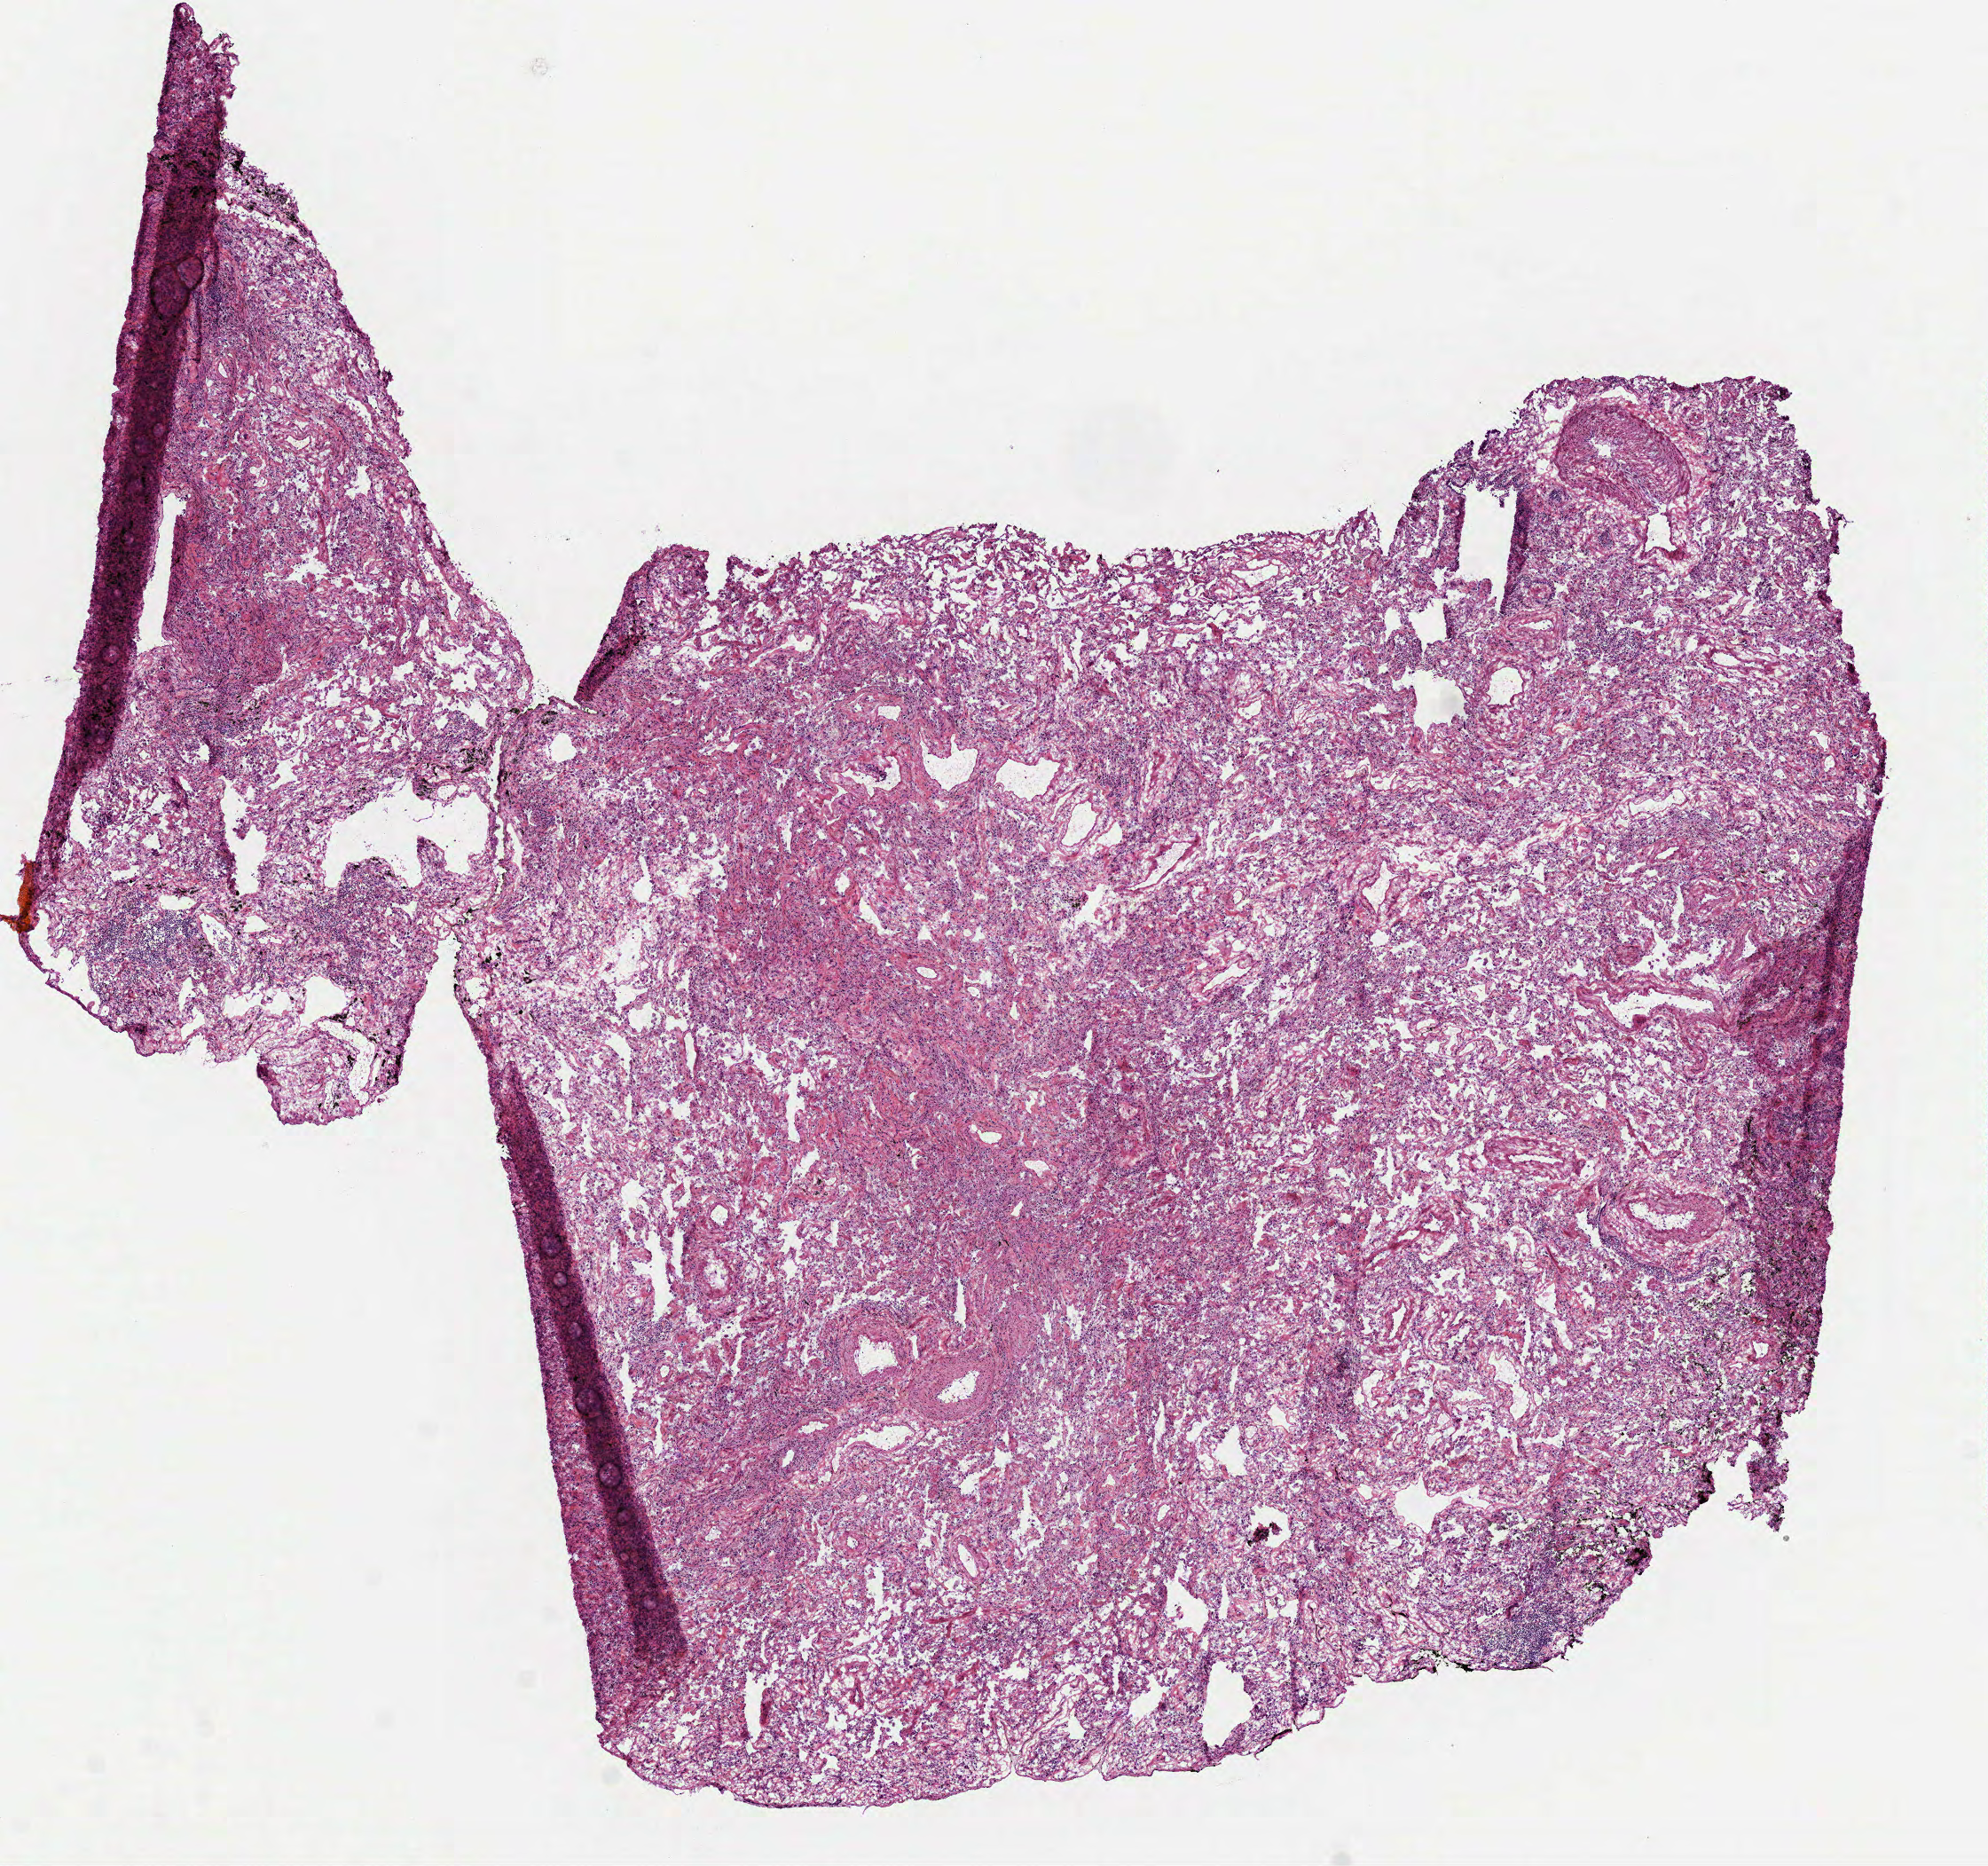
H&E whole-slide image, a low-resolution overview of the entire scanned area, about 9.0 x 8.5 mm (acquisition: 40x scan), frozen section from the top of the tissue portion, sample: primary tumour, lung. Female, age 75 years at initial diagnosis. Slide review estimates, as recorded: tumour cells 100%, tumour nuclei 61%, normal cells 0%, stromal cells 0%, necrosis 0%. Inflammatory infiltration, as recorded: lymphocyte infiltration 10%, monocyte infiltration 0%, neutrophil infiltration 5%.
• AJCC pathologic stage: IA
• laterality: right
• histologic diagnosis: Squamous cell carcinoma, large cell, nonkeratinizing, NOS